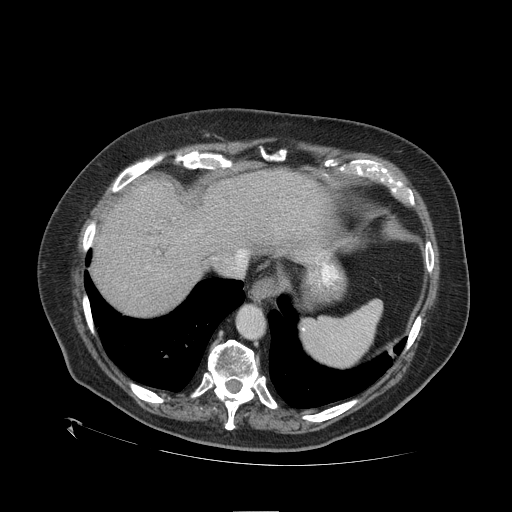
Contrast-enhanced abdominal CT (liver protocol), one axial slice. Position 90 of 109 along the scan axis. Reconstruction kernel STANDARD. 120 kVp. One of 2 acquisitions stored at this slice position. Soft-tissue window (W 400 / L 40 HU). 2.5 mm slice thickness. 512 × 512 image matrix, field of view 460 × 460 mm. From the clinical record (not read from this slice): diagnosis: hepatocellular carcinoma (patient treated with transarterial chemoembolisation; whether this scan precedes or follows treatment is not stated here); TNM stage (as recorded): Stage-I; Child-Pugh class: A.
Outlined on this slice (semi-automatic segmentation, software-assisted and operator-edited):
- abdominal aorta: bounding box [x1, y1, x2, y2] px = [238, 307, 264, 337]
- liver parenchyma outside the tumour (the mass and vessels are separate outlines, so this box may not span the whole liver): [92, 168, 346, 316]